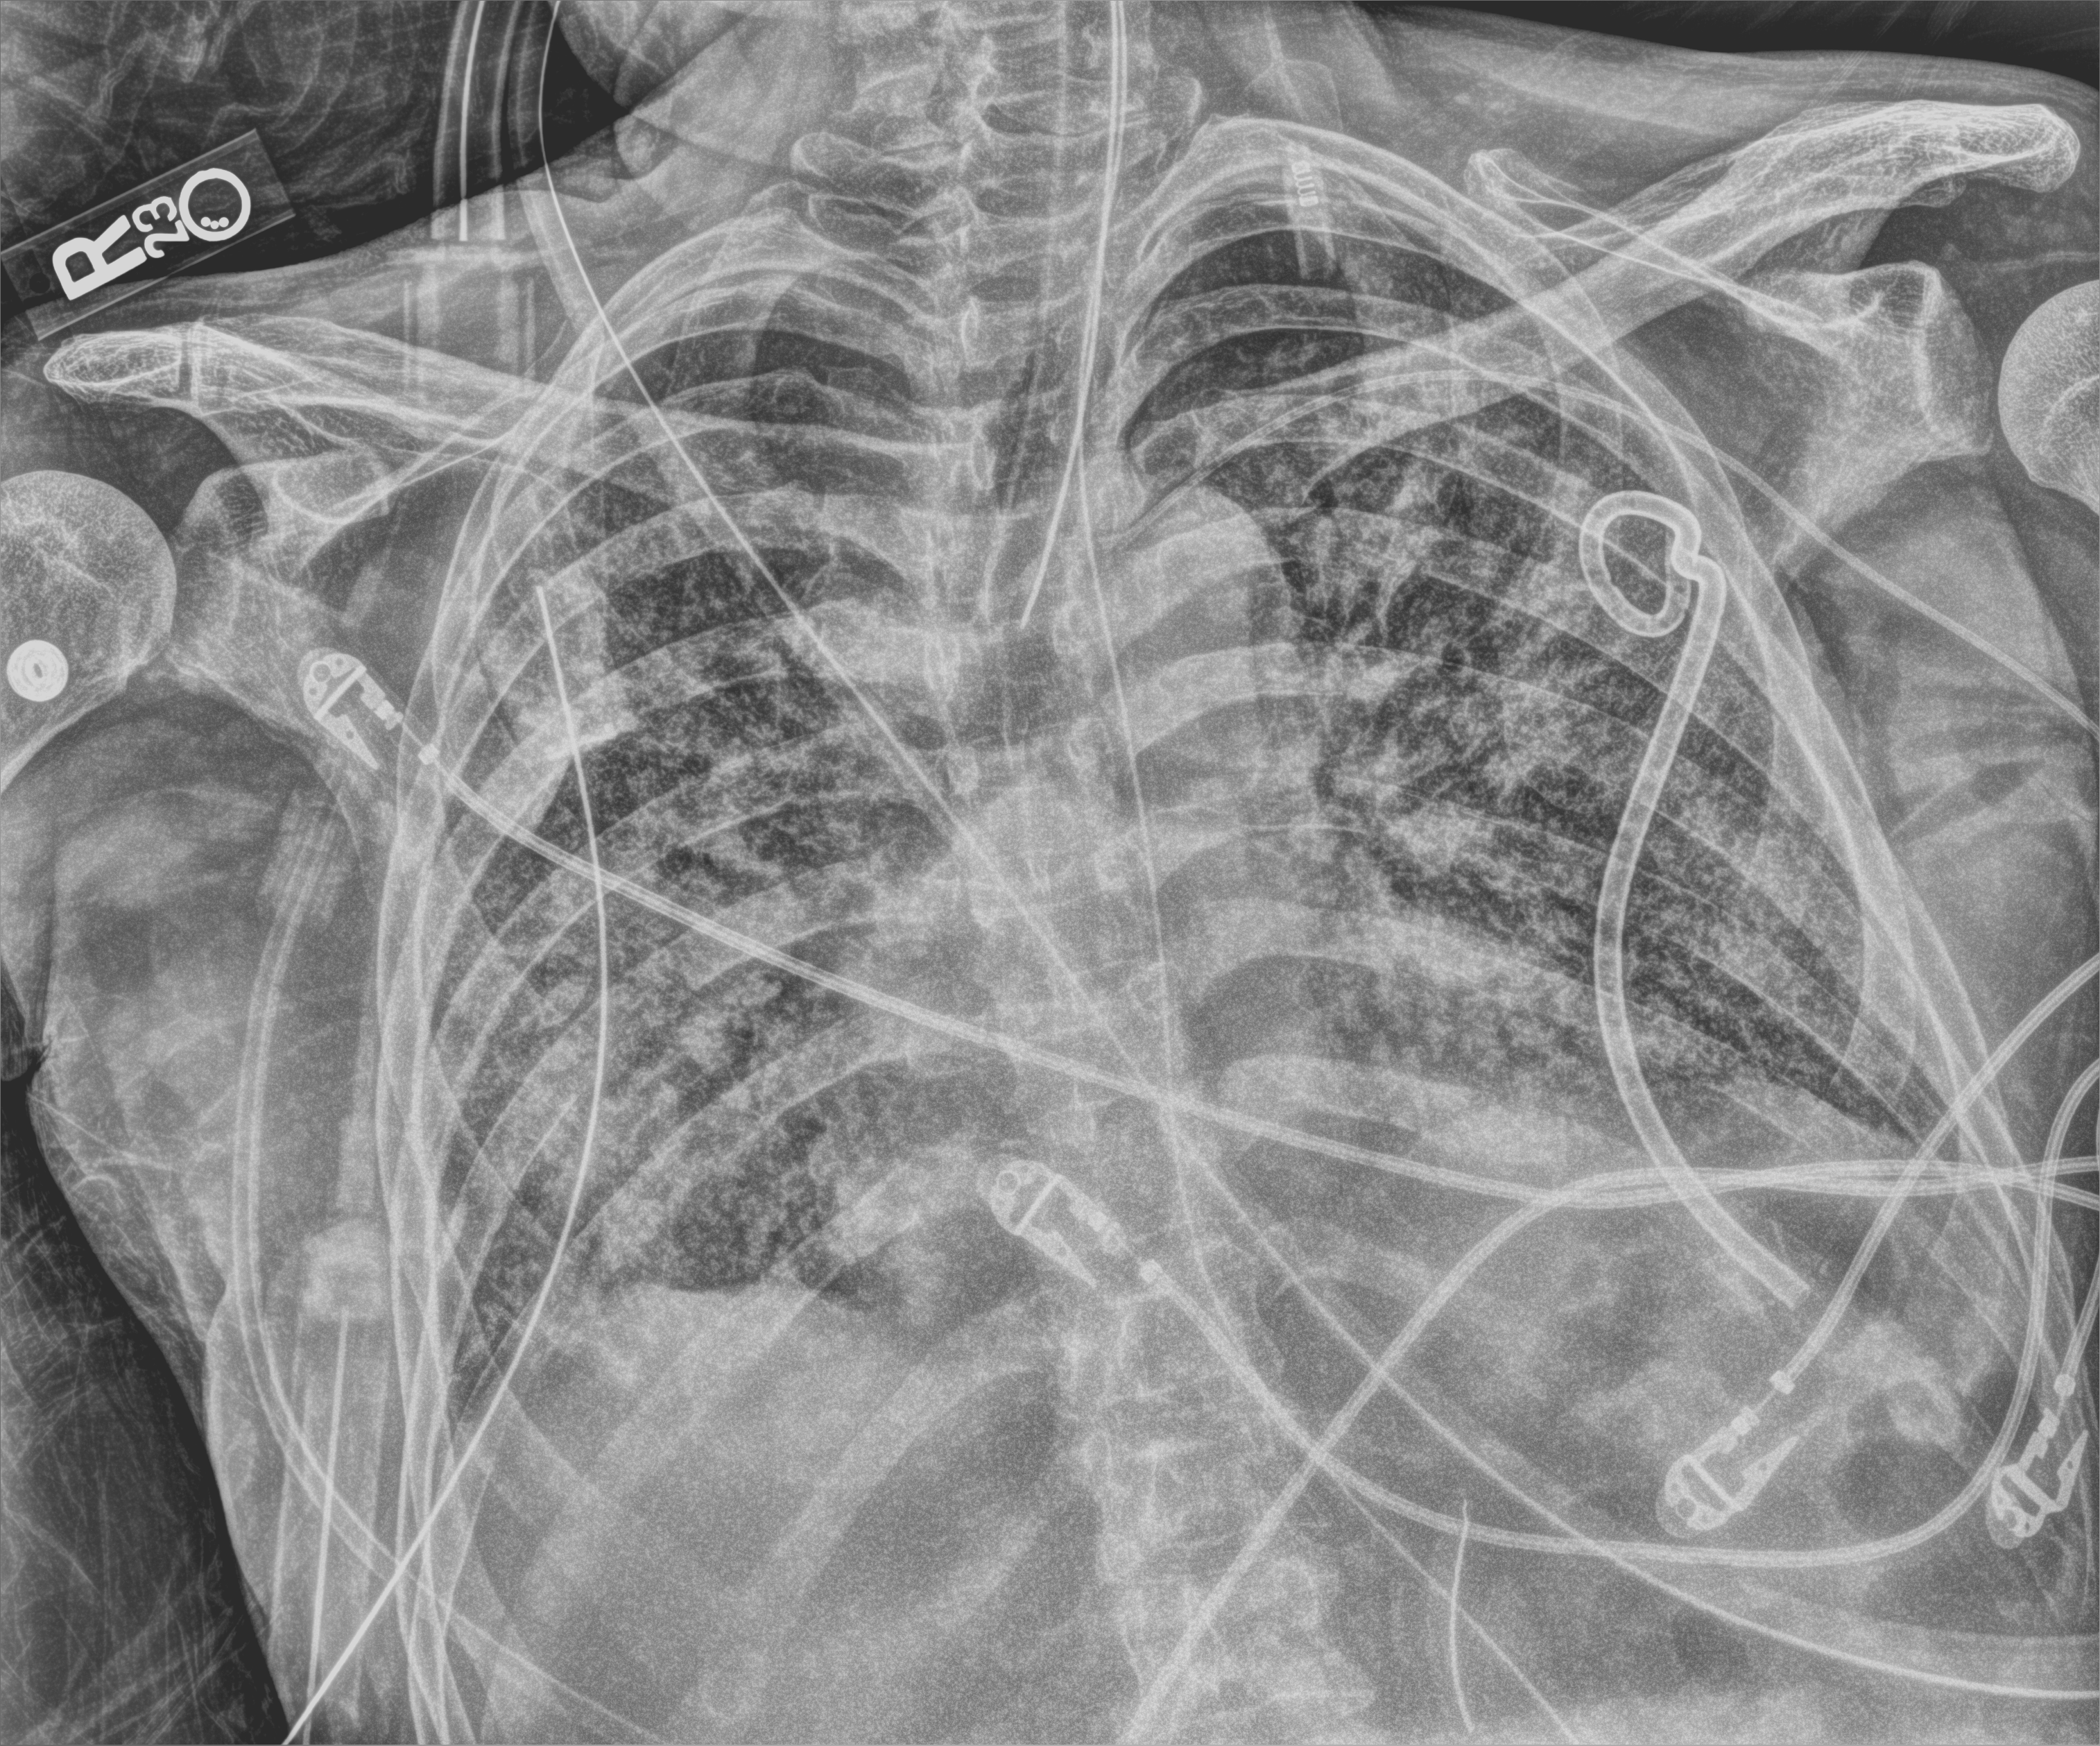
Bedside chest radiograph (computed radiography). Male patient hospitalised with COVID-19, age 60–74 years.
From the hospital-stay record, not from the radiograph (when in the stay this image was taken is not recorded): admitted to intensive care during this hospital stay: yes; mechanically ventilated during this hospital stay: yes.